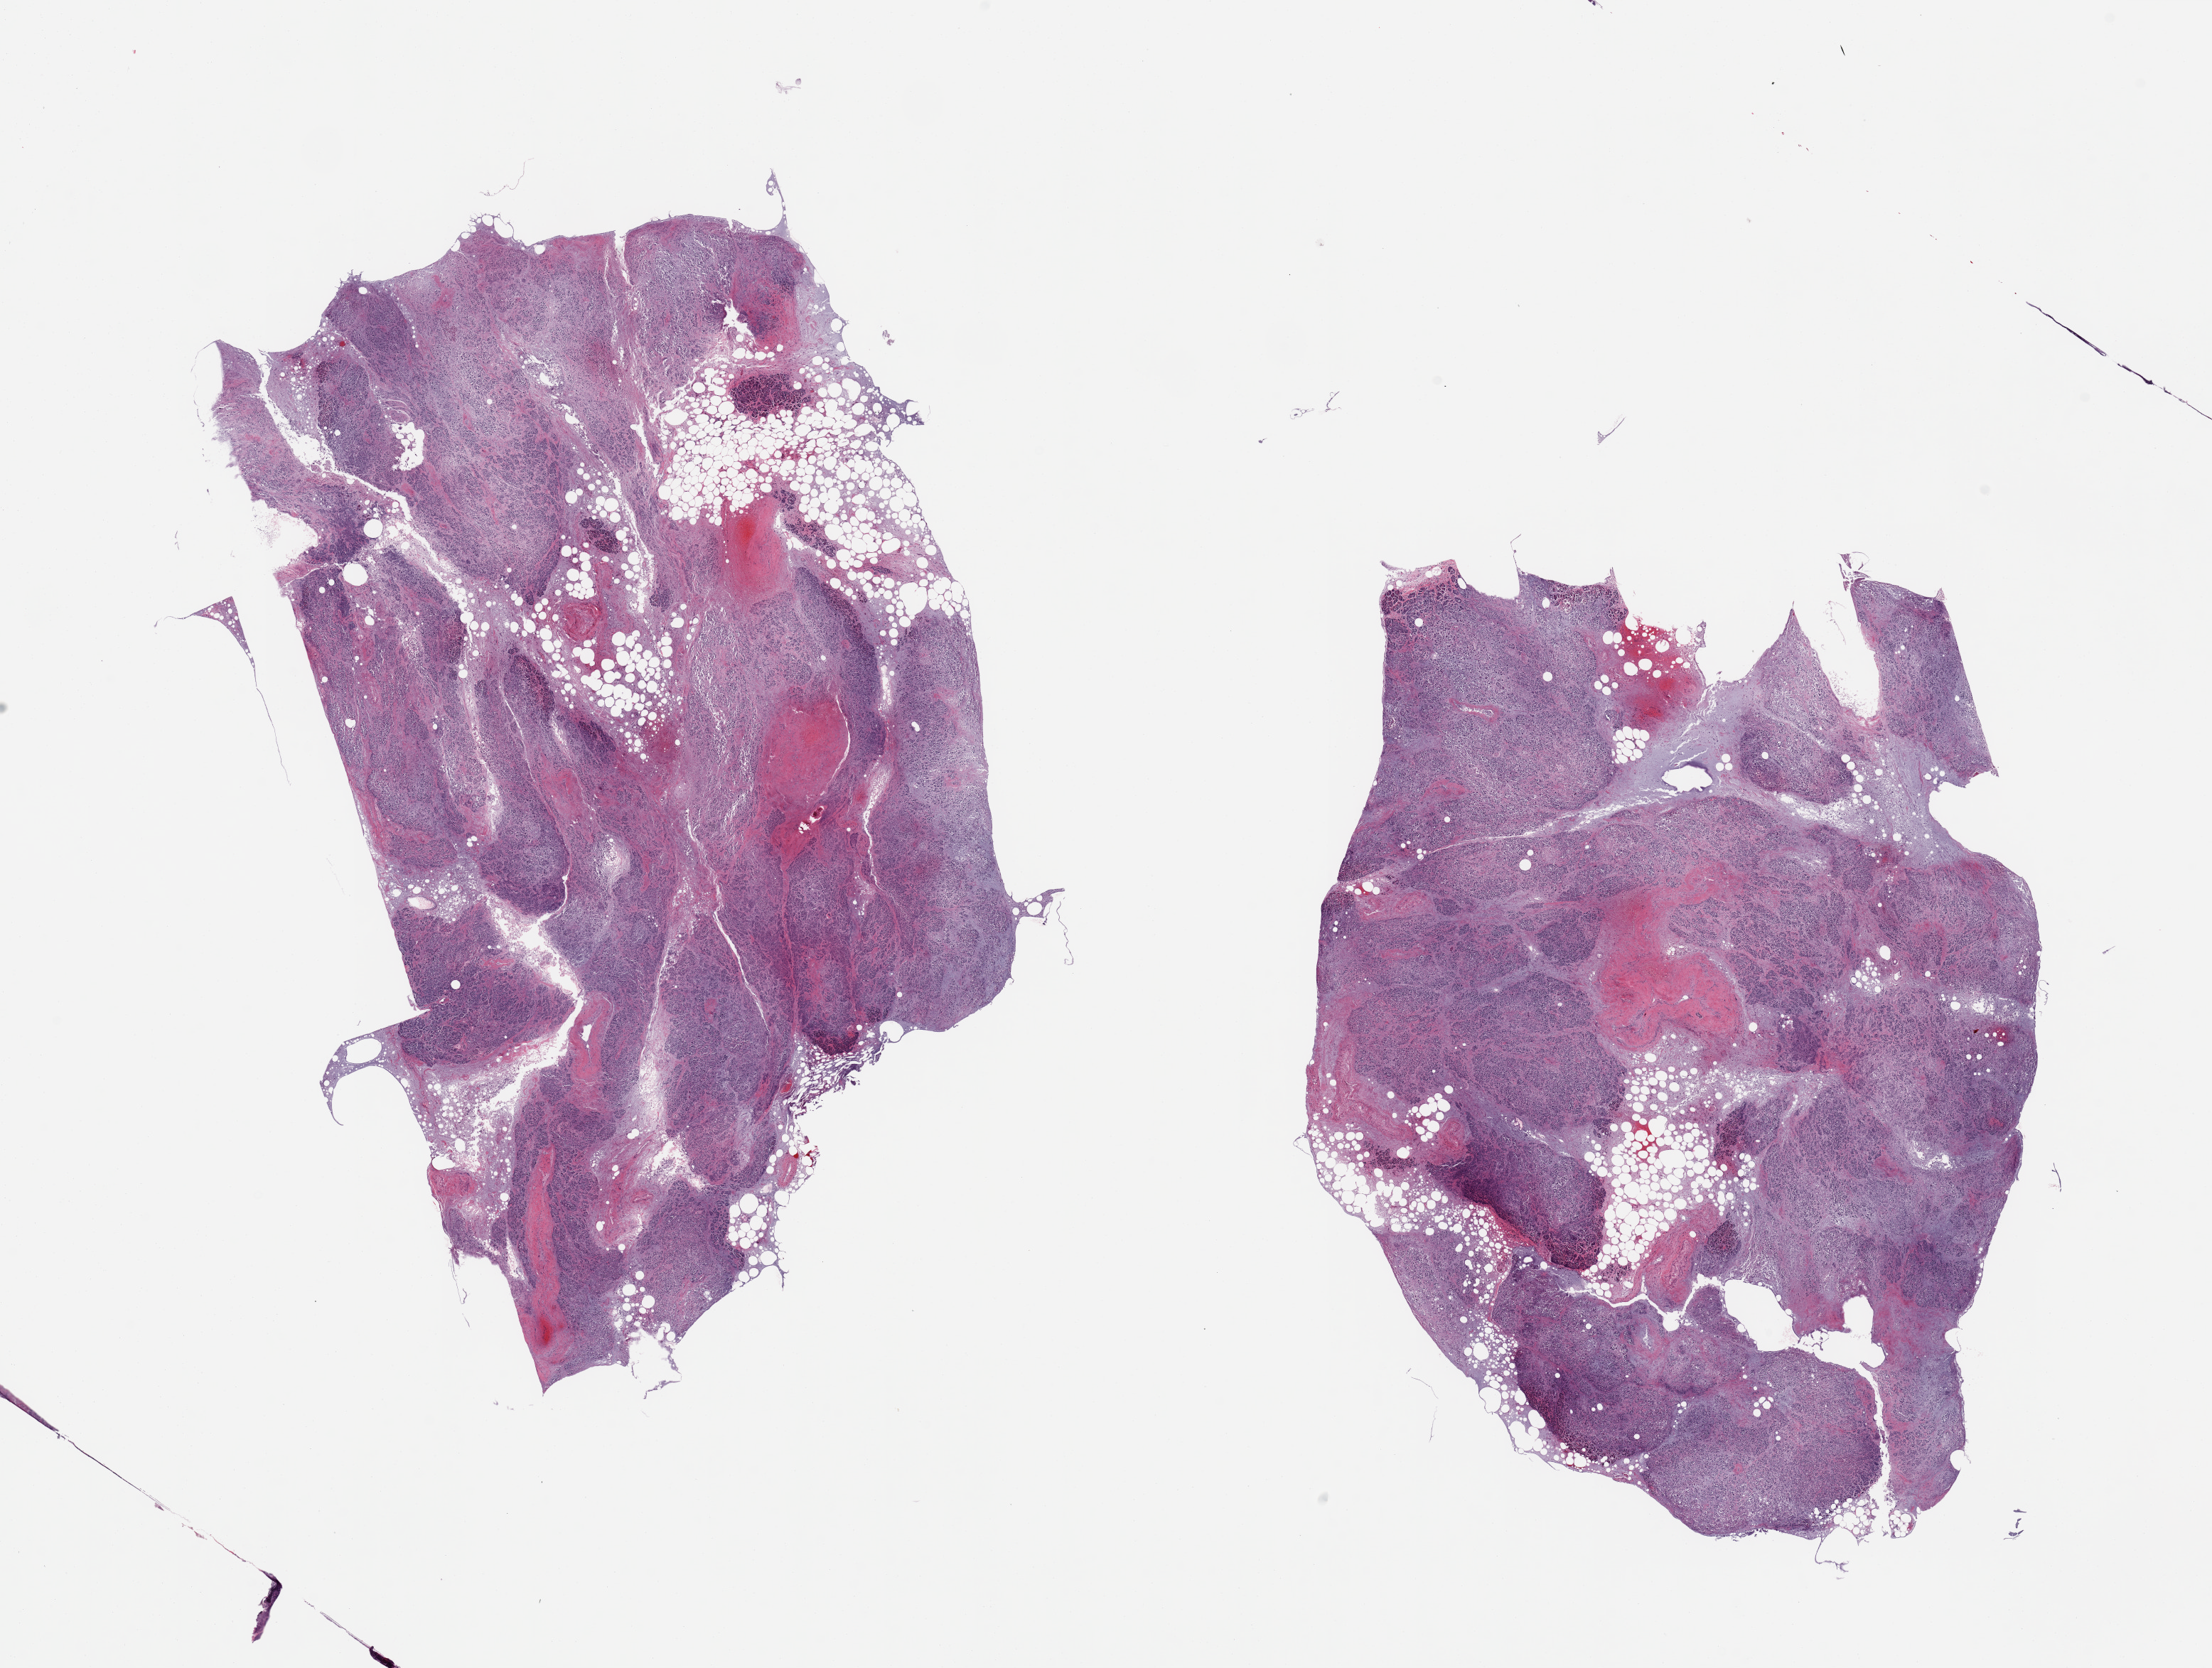
Hematoxylin and eosin (H&E) whole-slide image, brightfield — low-resolution overview of the scanned area, about 24.6 x 18.6 mm (acquisition: 20x scan); PAXgene-fixed paraffin-embedded (PFPE) section; target tissue: pancreas; donor tissue sample. Donor sex: male.
- reviewer comment on this tissue sample: 2 pieces, advanced saponification